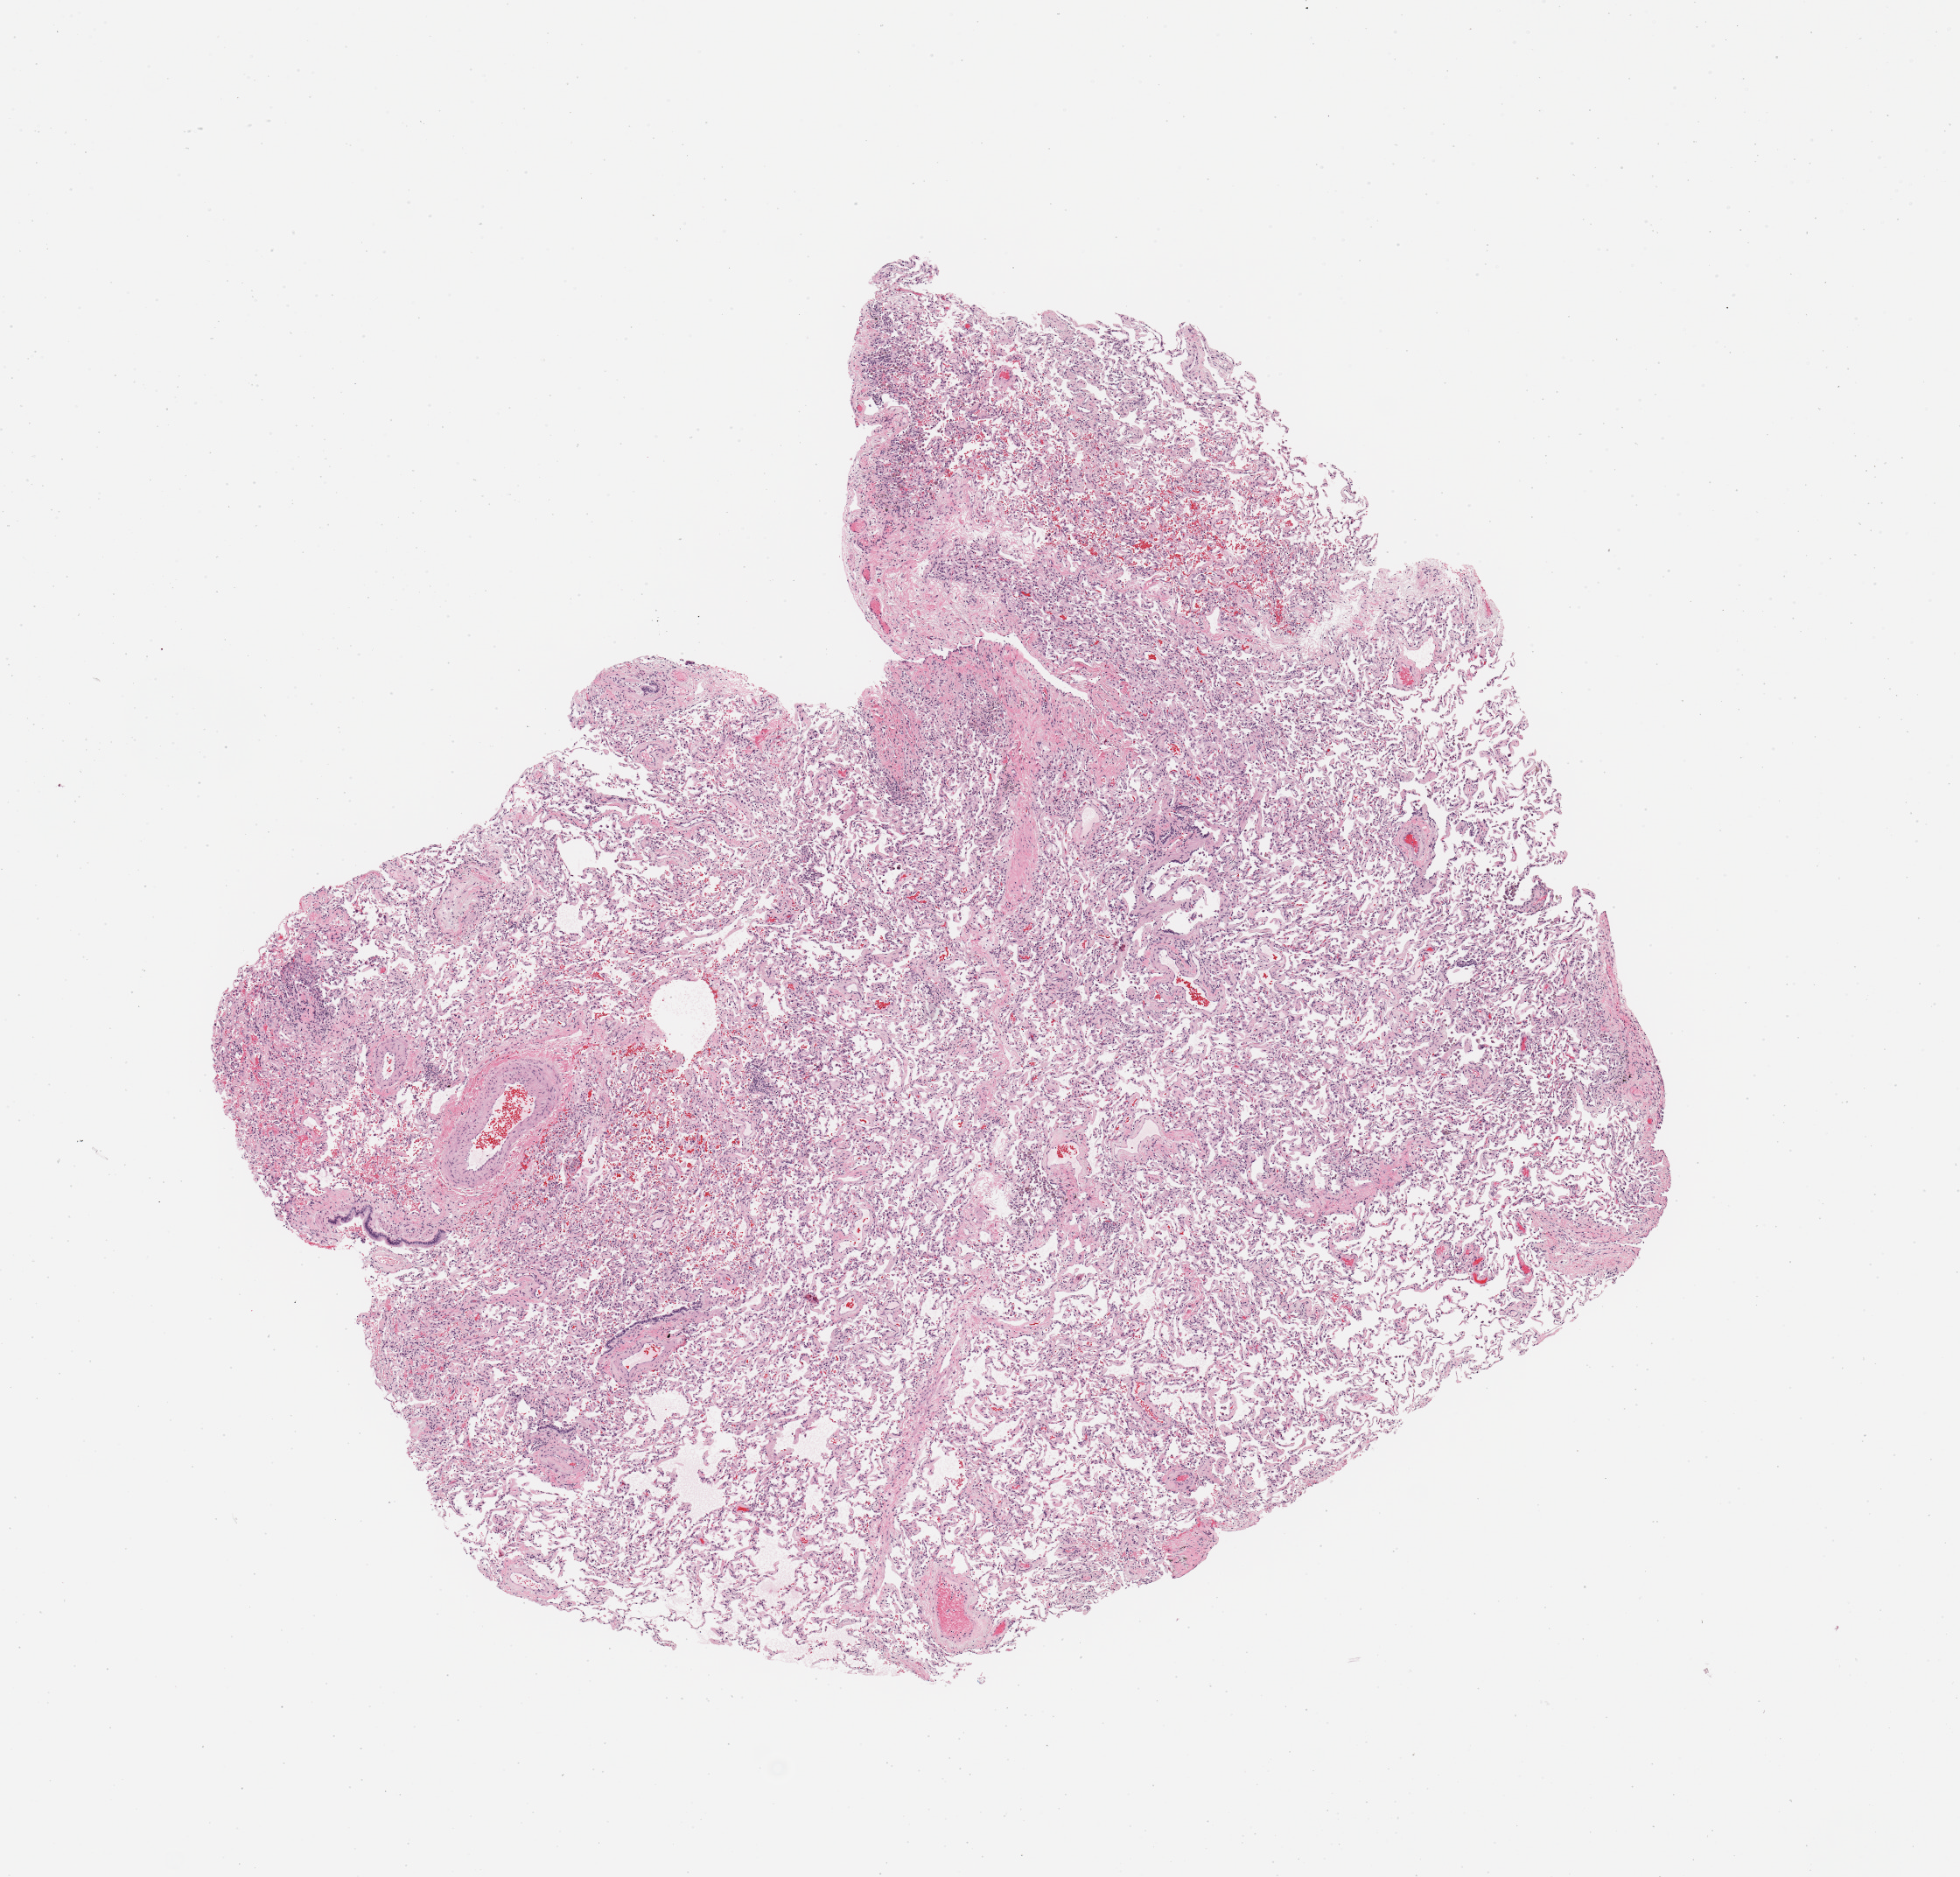
Digitized Hematoxylin and eosin (H&E) stained tissue section (whole slide) — shown as a low-resolution overview of the whole scanned area (about 8.9 x 8.5 mm), normal (non-tumour) tissue sample, sampled site: lung. Female, 67 y/o.
This section: normal (non-tumour) tissue from the same patient. Patient diagnosis: Adenocarcinoma, NOS.